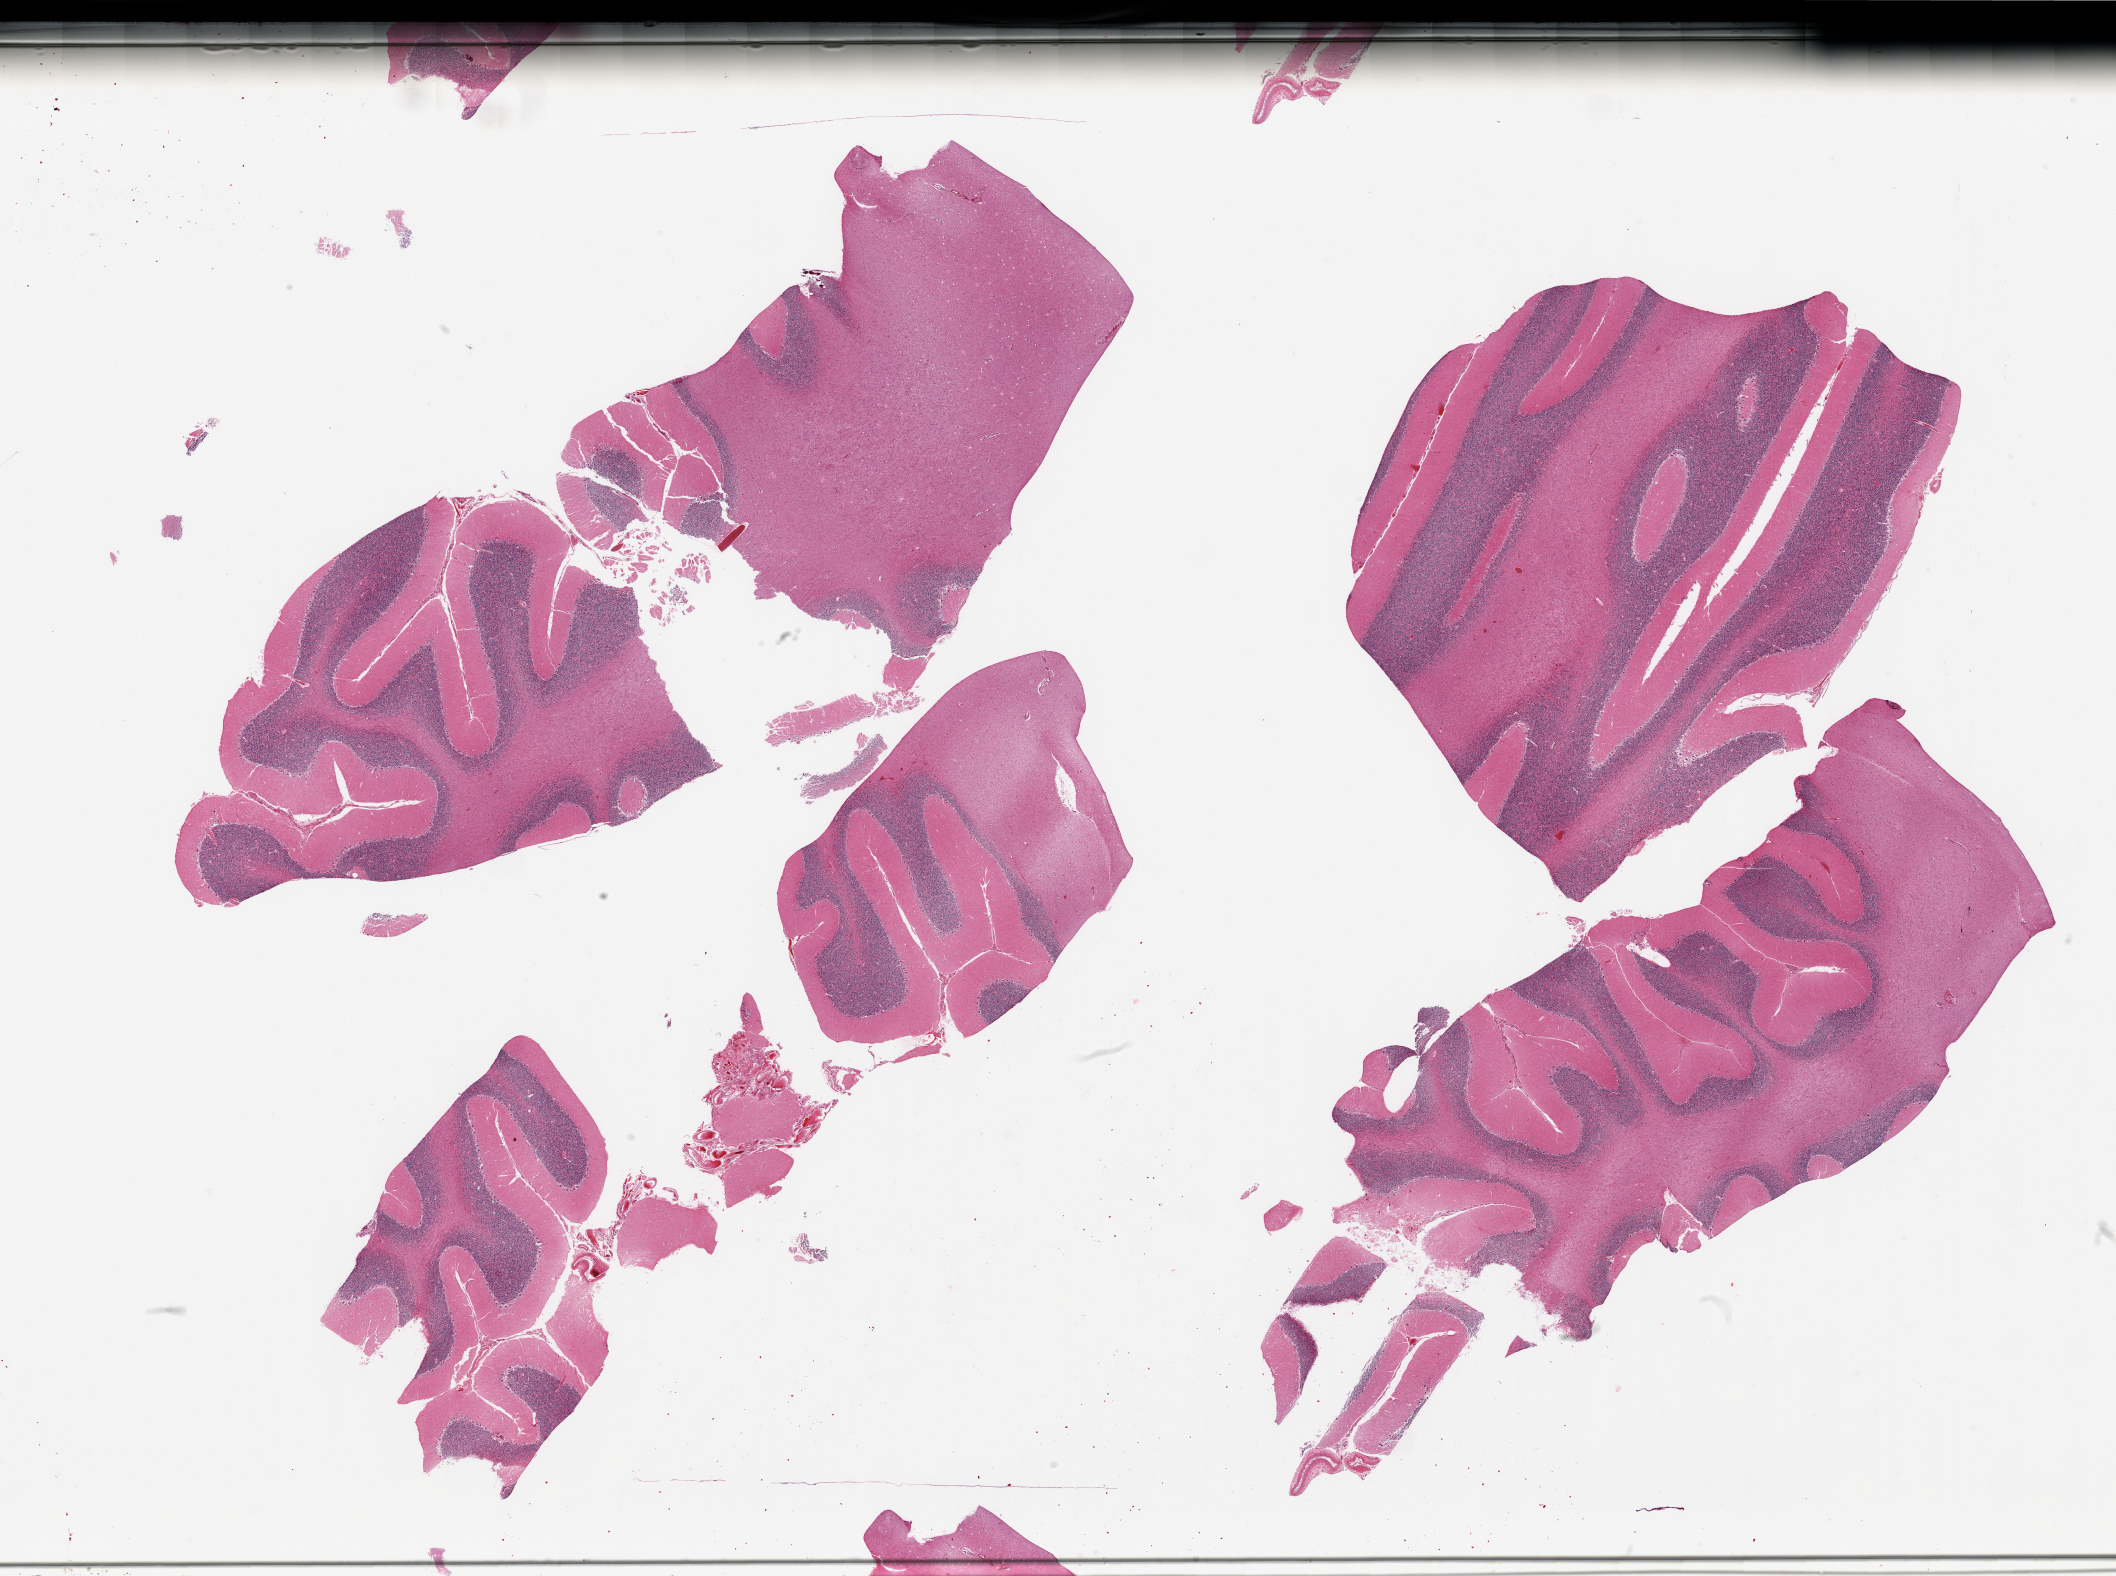
Digitized haematoxylin and eosin-stained section — a low-resolution overview of the entire scanned area, about 33.5 x 24.9 mm; PAXgene-fixed paraffin-embedded (PFPE) section; section of cerebellum (target tissue); tissue donor sample. Male donor.
Review note (as recorded): 4 fragmented pieces.